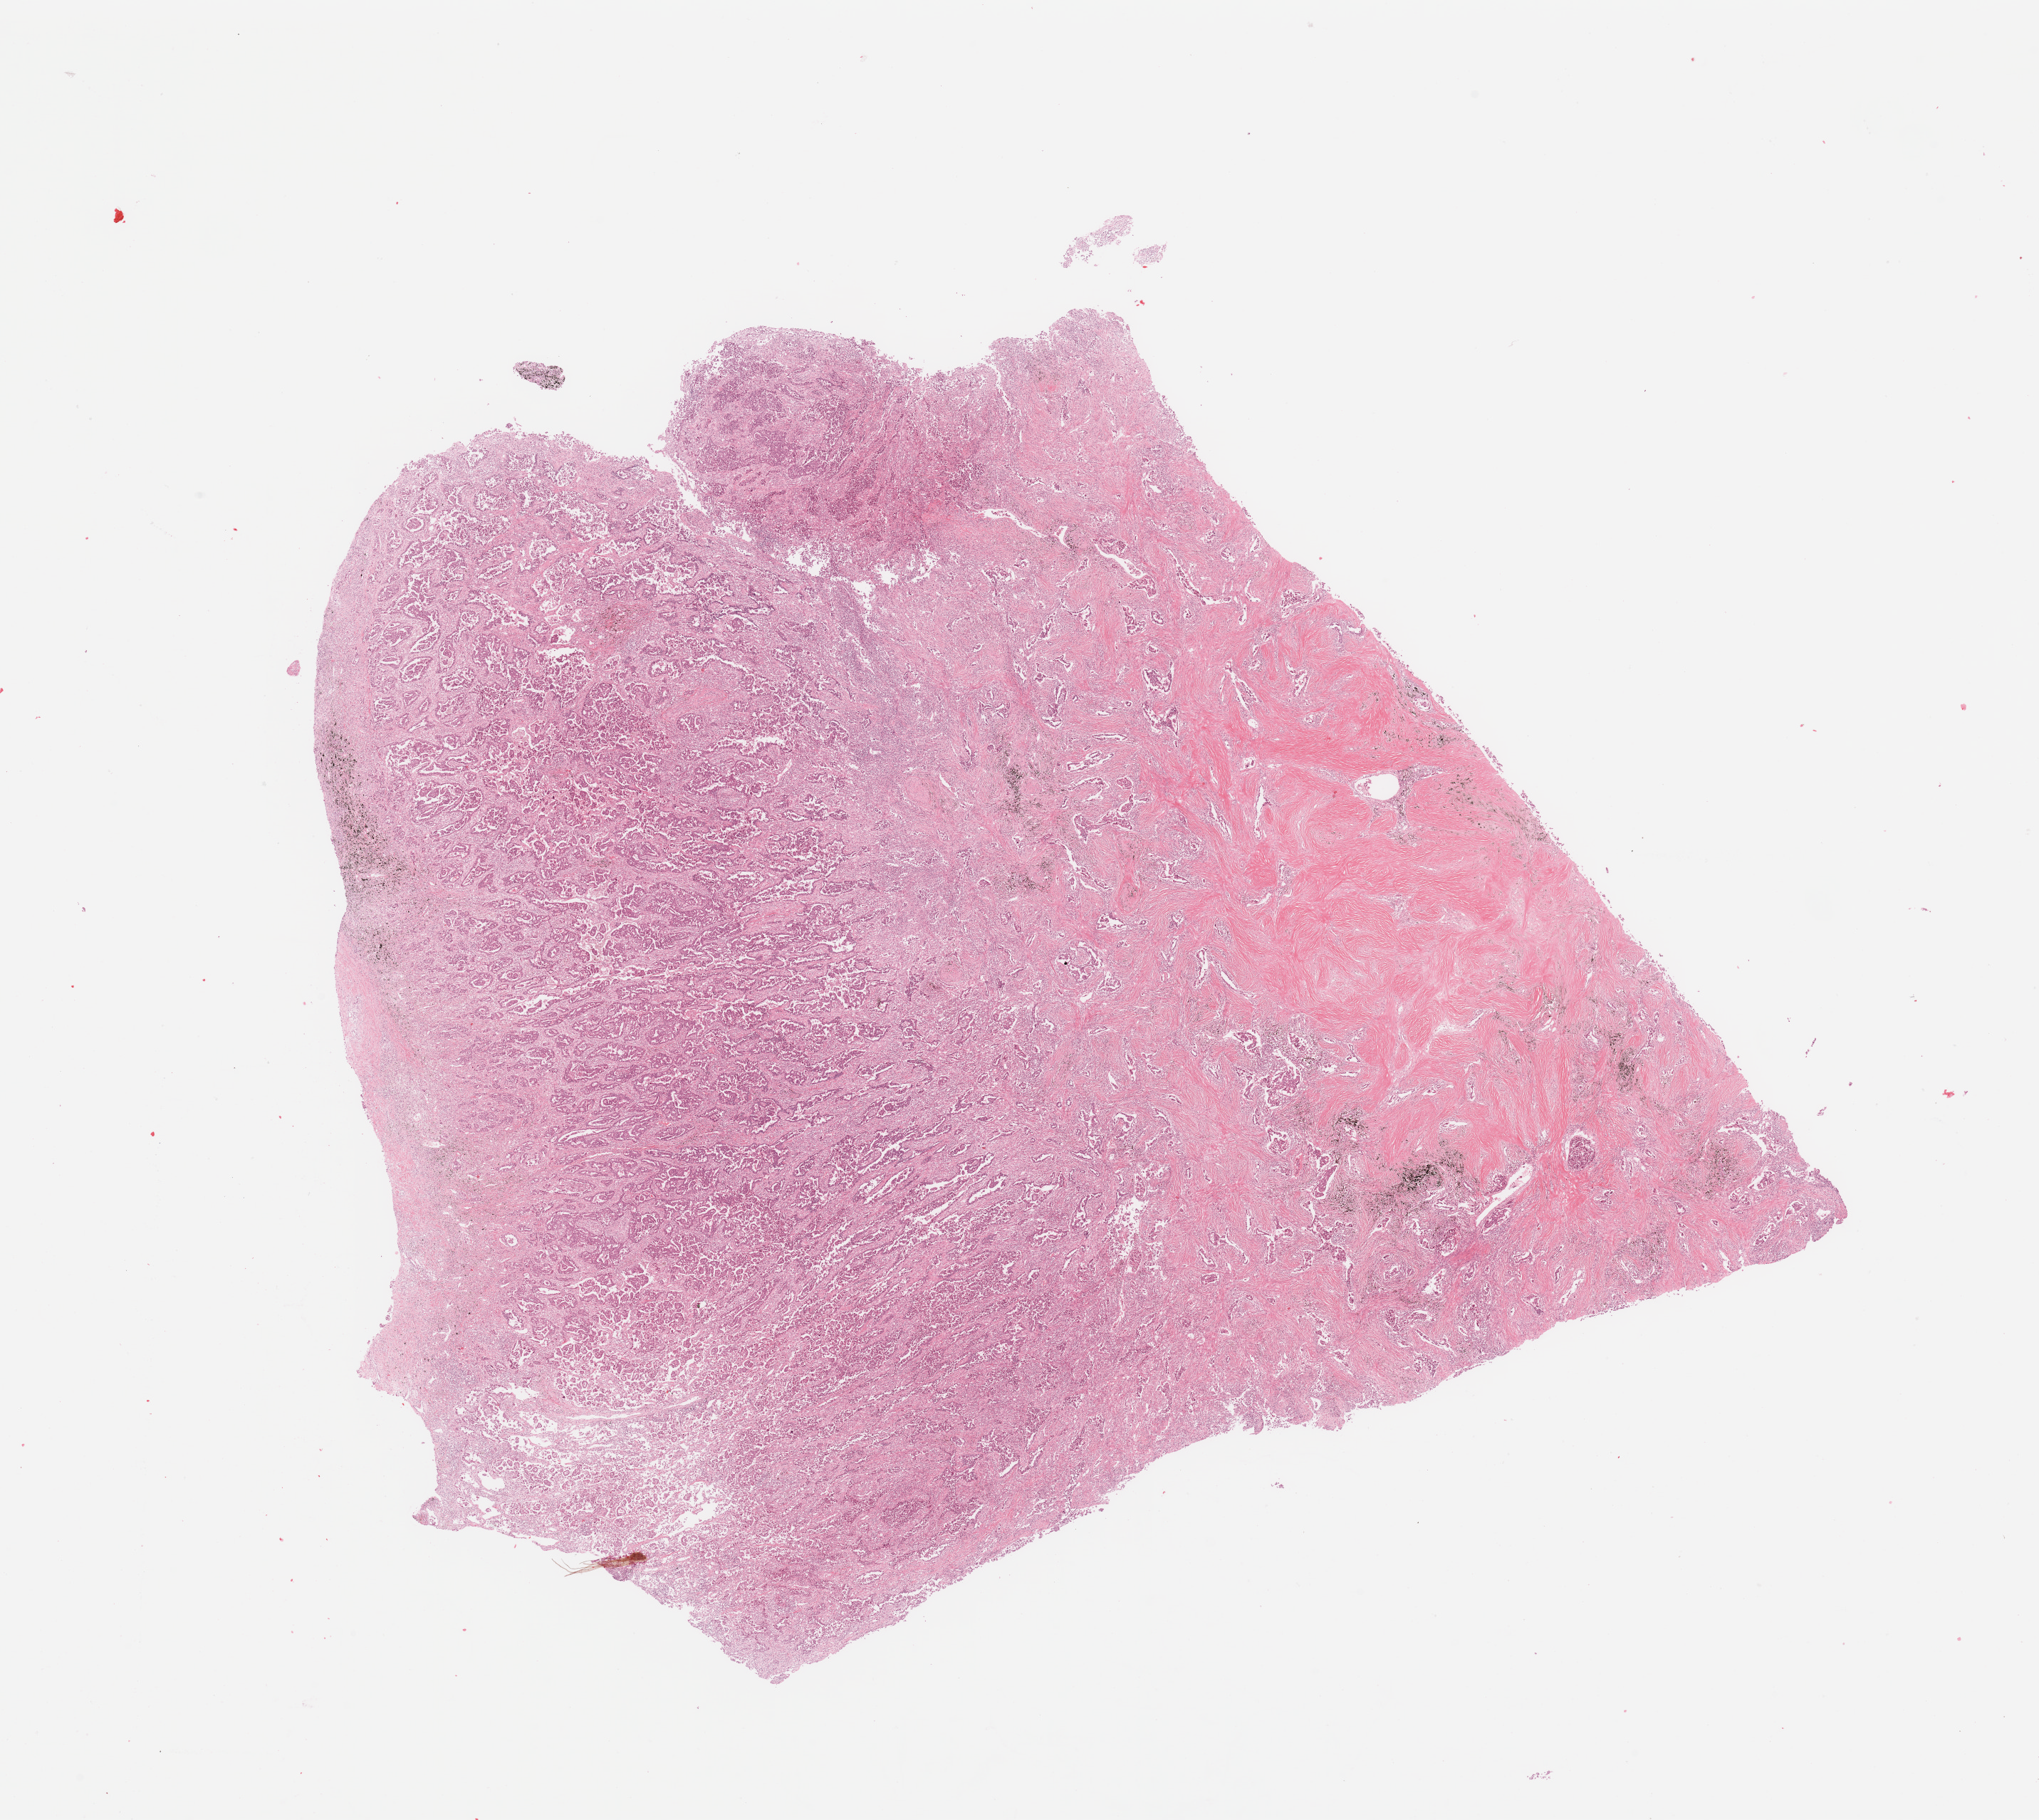
Hematoxylin and eosin (H&E) stained whole-slide image — whole scanned area (about 22.6 x 20.2 mm, from a 20x scan) shown as a low-resolution overview. Lung, tumour tissue. 62-year-old male patient. Histologic grade: G3 (poorly differentiated).
Primary tumour site (as recorded): left upper lobe. Diagnosis: Adenocarcinoma, NOS. AJCC pathologic stage: IIIA.